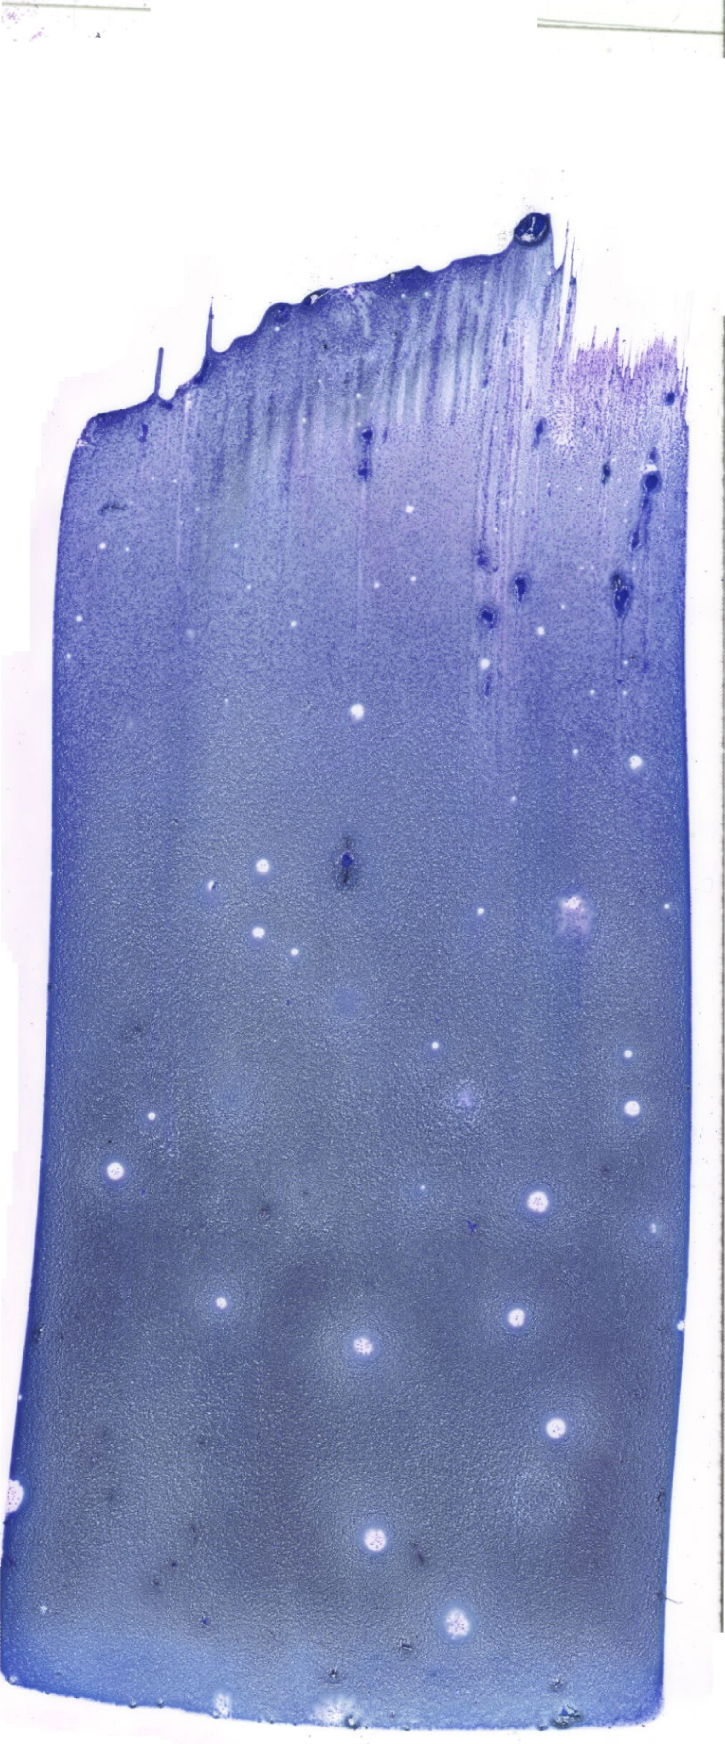
May-Grünwald–Giemsa-stained marrow aspirate smear (whole slide), a low-resolution overview of the entire scanned area, about 20.6 x 49.4 mm. Male patient.
Diagnosis: Acute Myelomonocytic Leukemia with Abnormal Eosinophils.